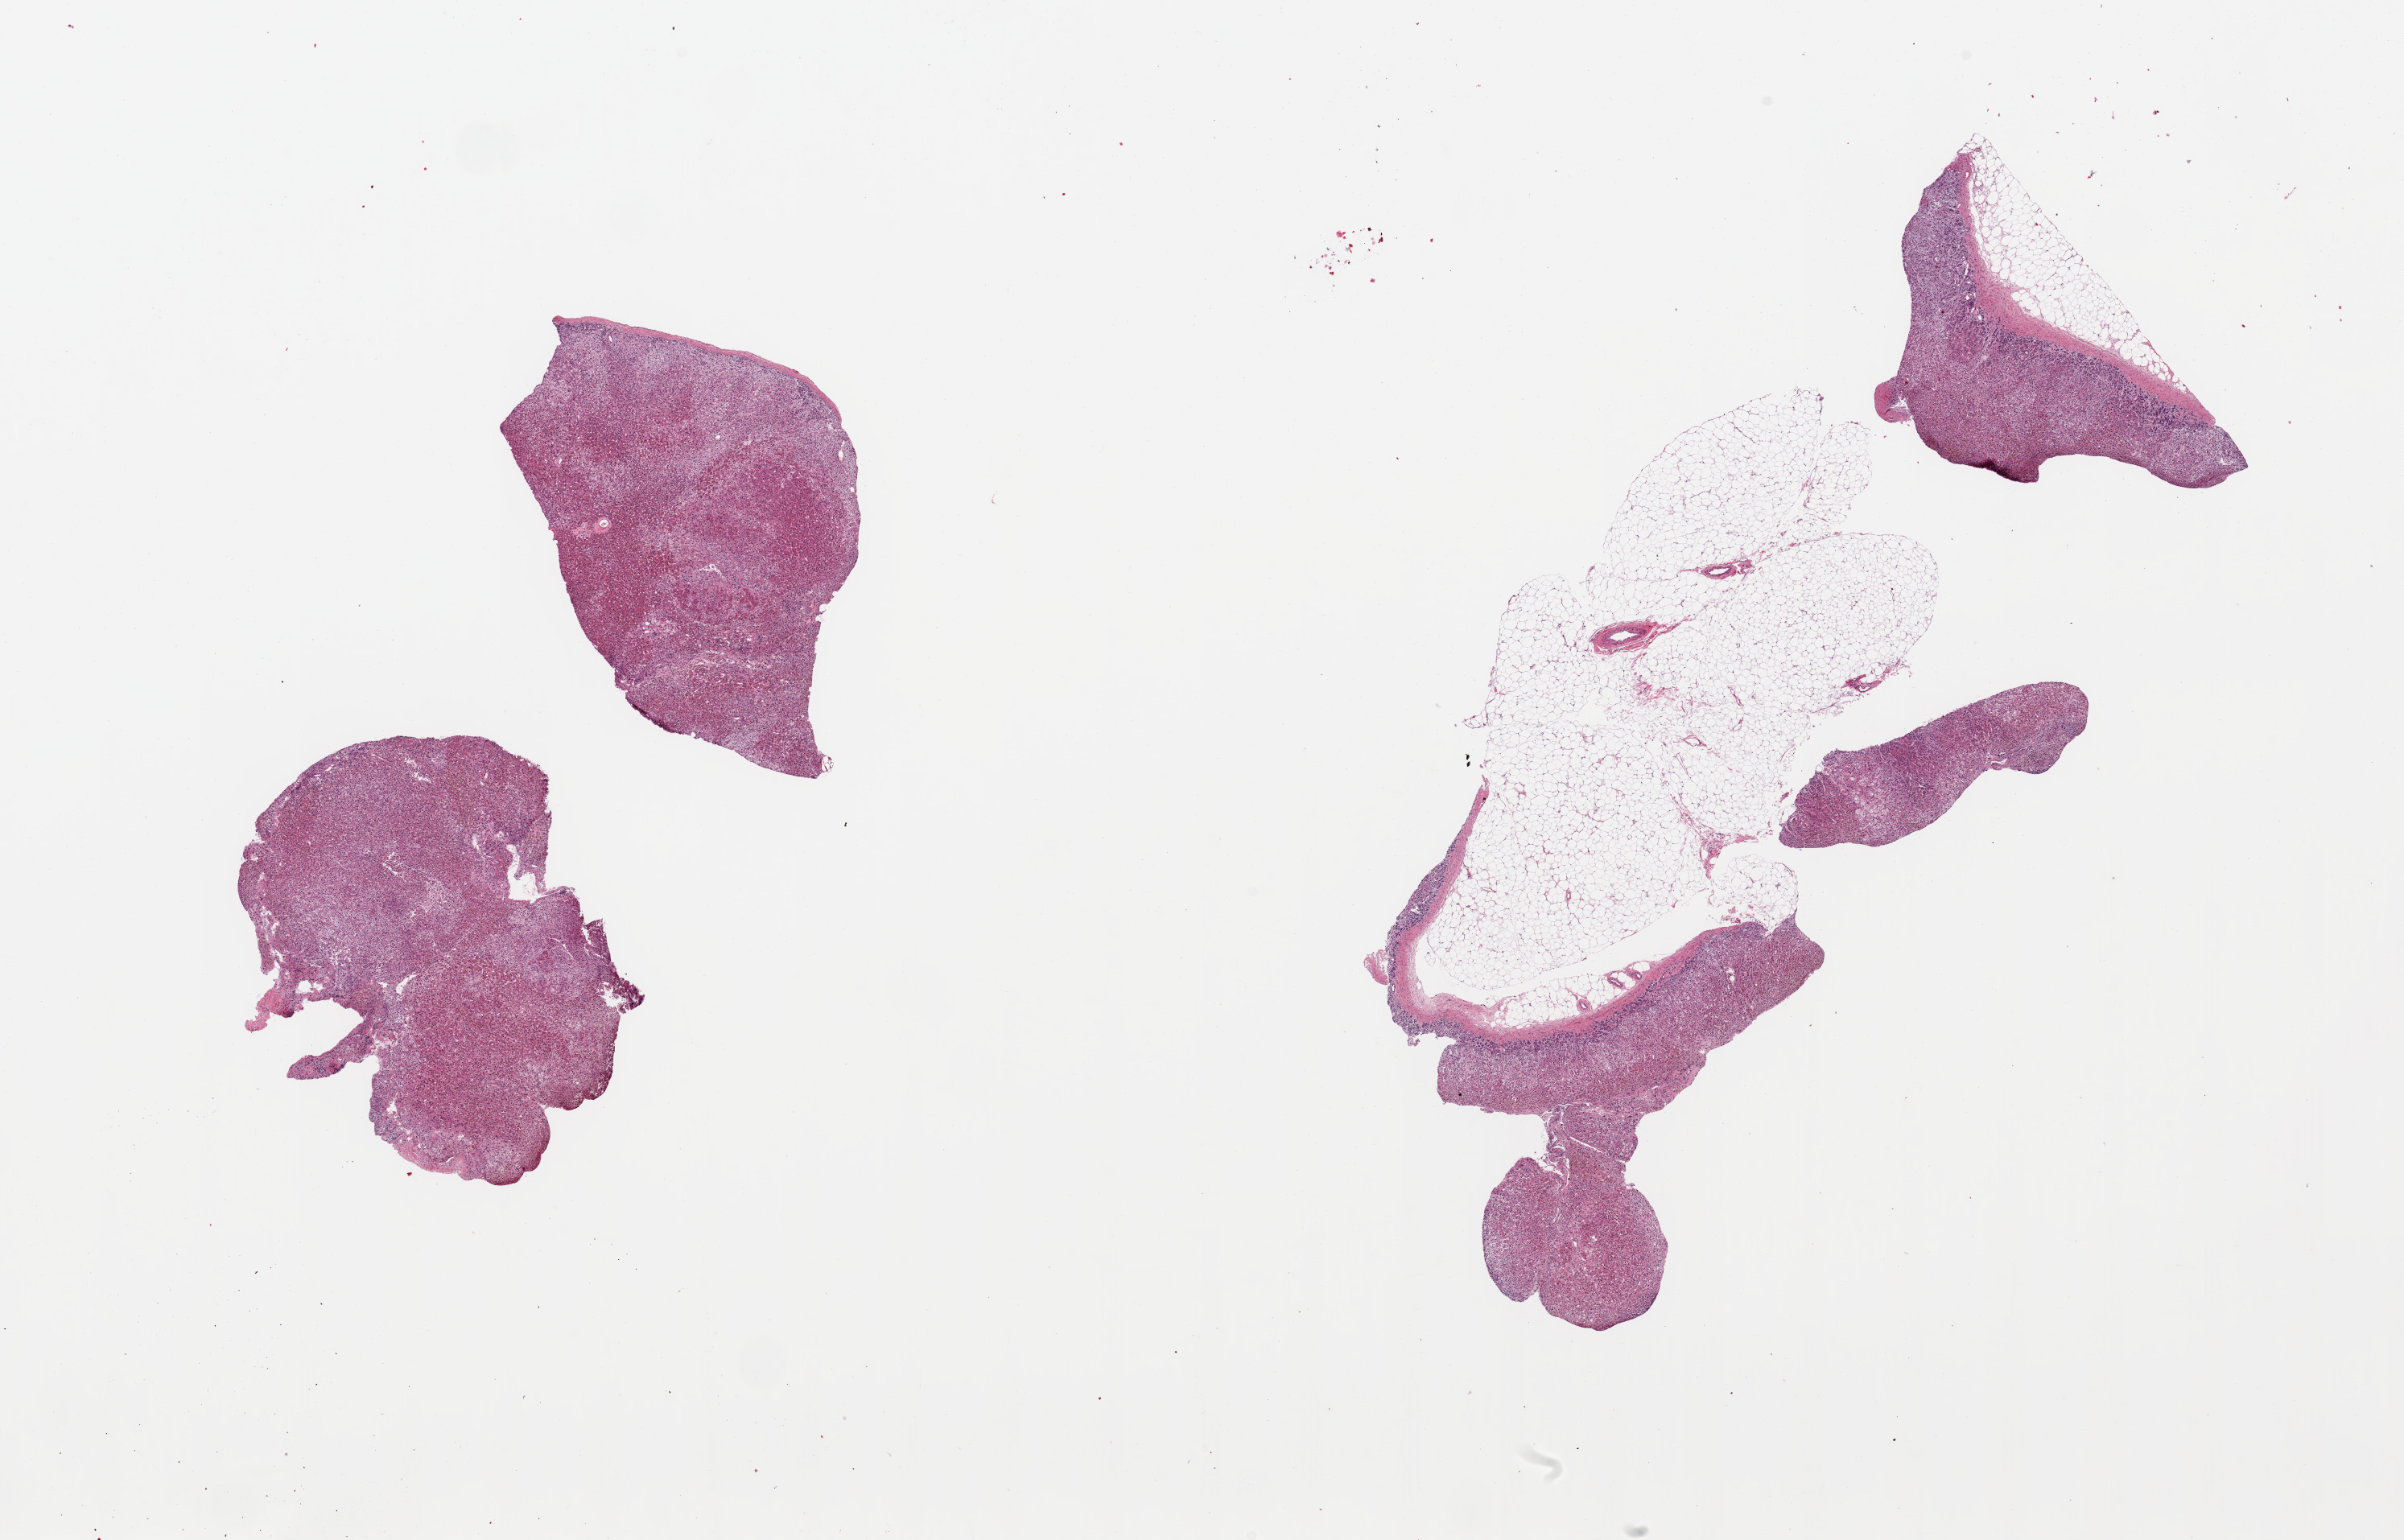
Digitized hematoxylin and eosin (H&E)-stained section, brightfield, a low-resolution overview of the entire scanned area, about 23.6 x 15.1 mm; PAXgene-fixed paraffin-embedded (PFPE) section; sampled site (target tissue): adrenal gland; donor tissue sample. Donor sex: male.
Reviewer comment on this tissue sample: 4 pieces; 1 piece with 70% fat.